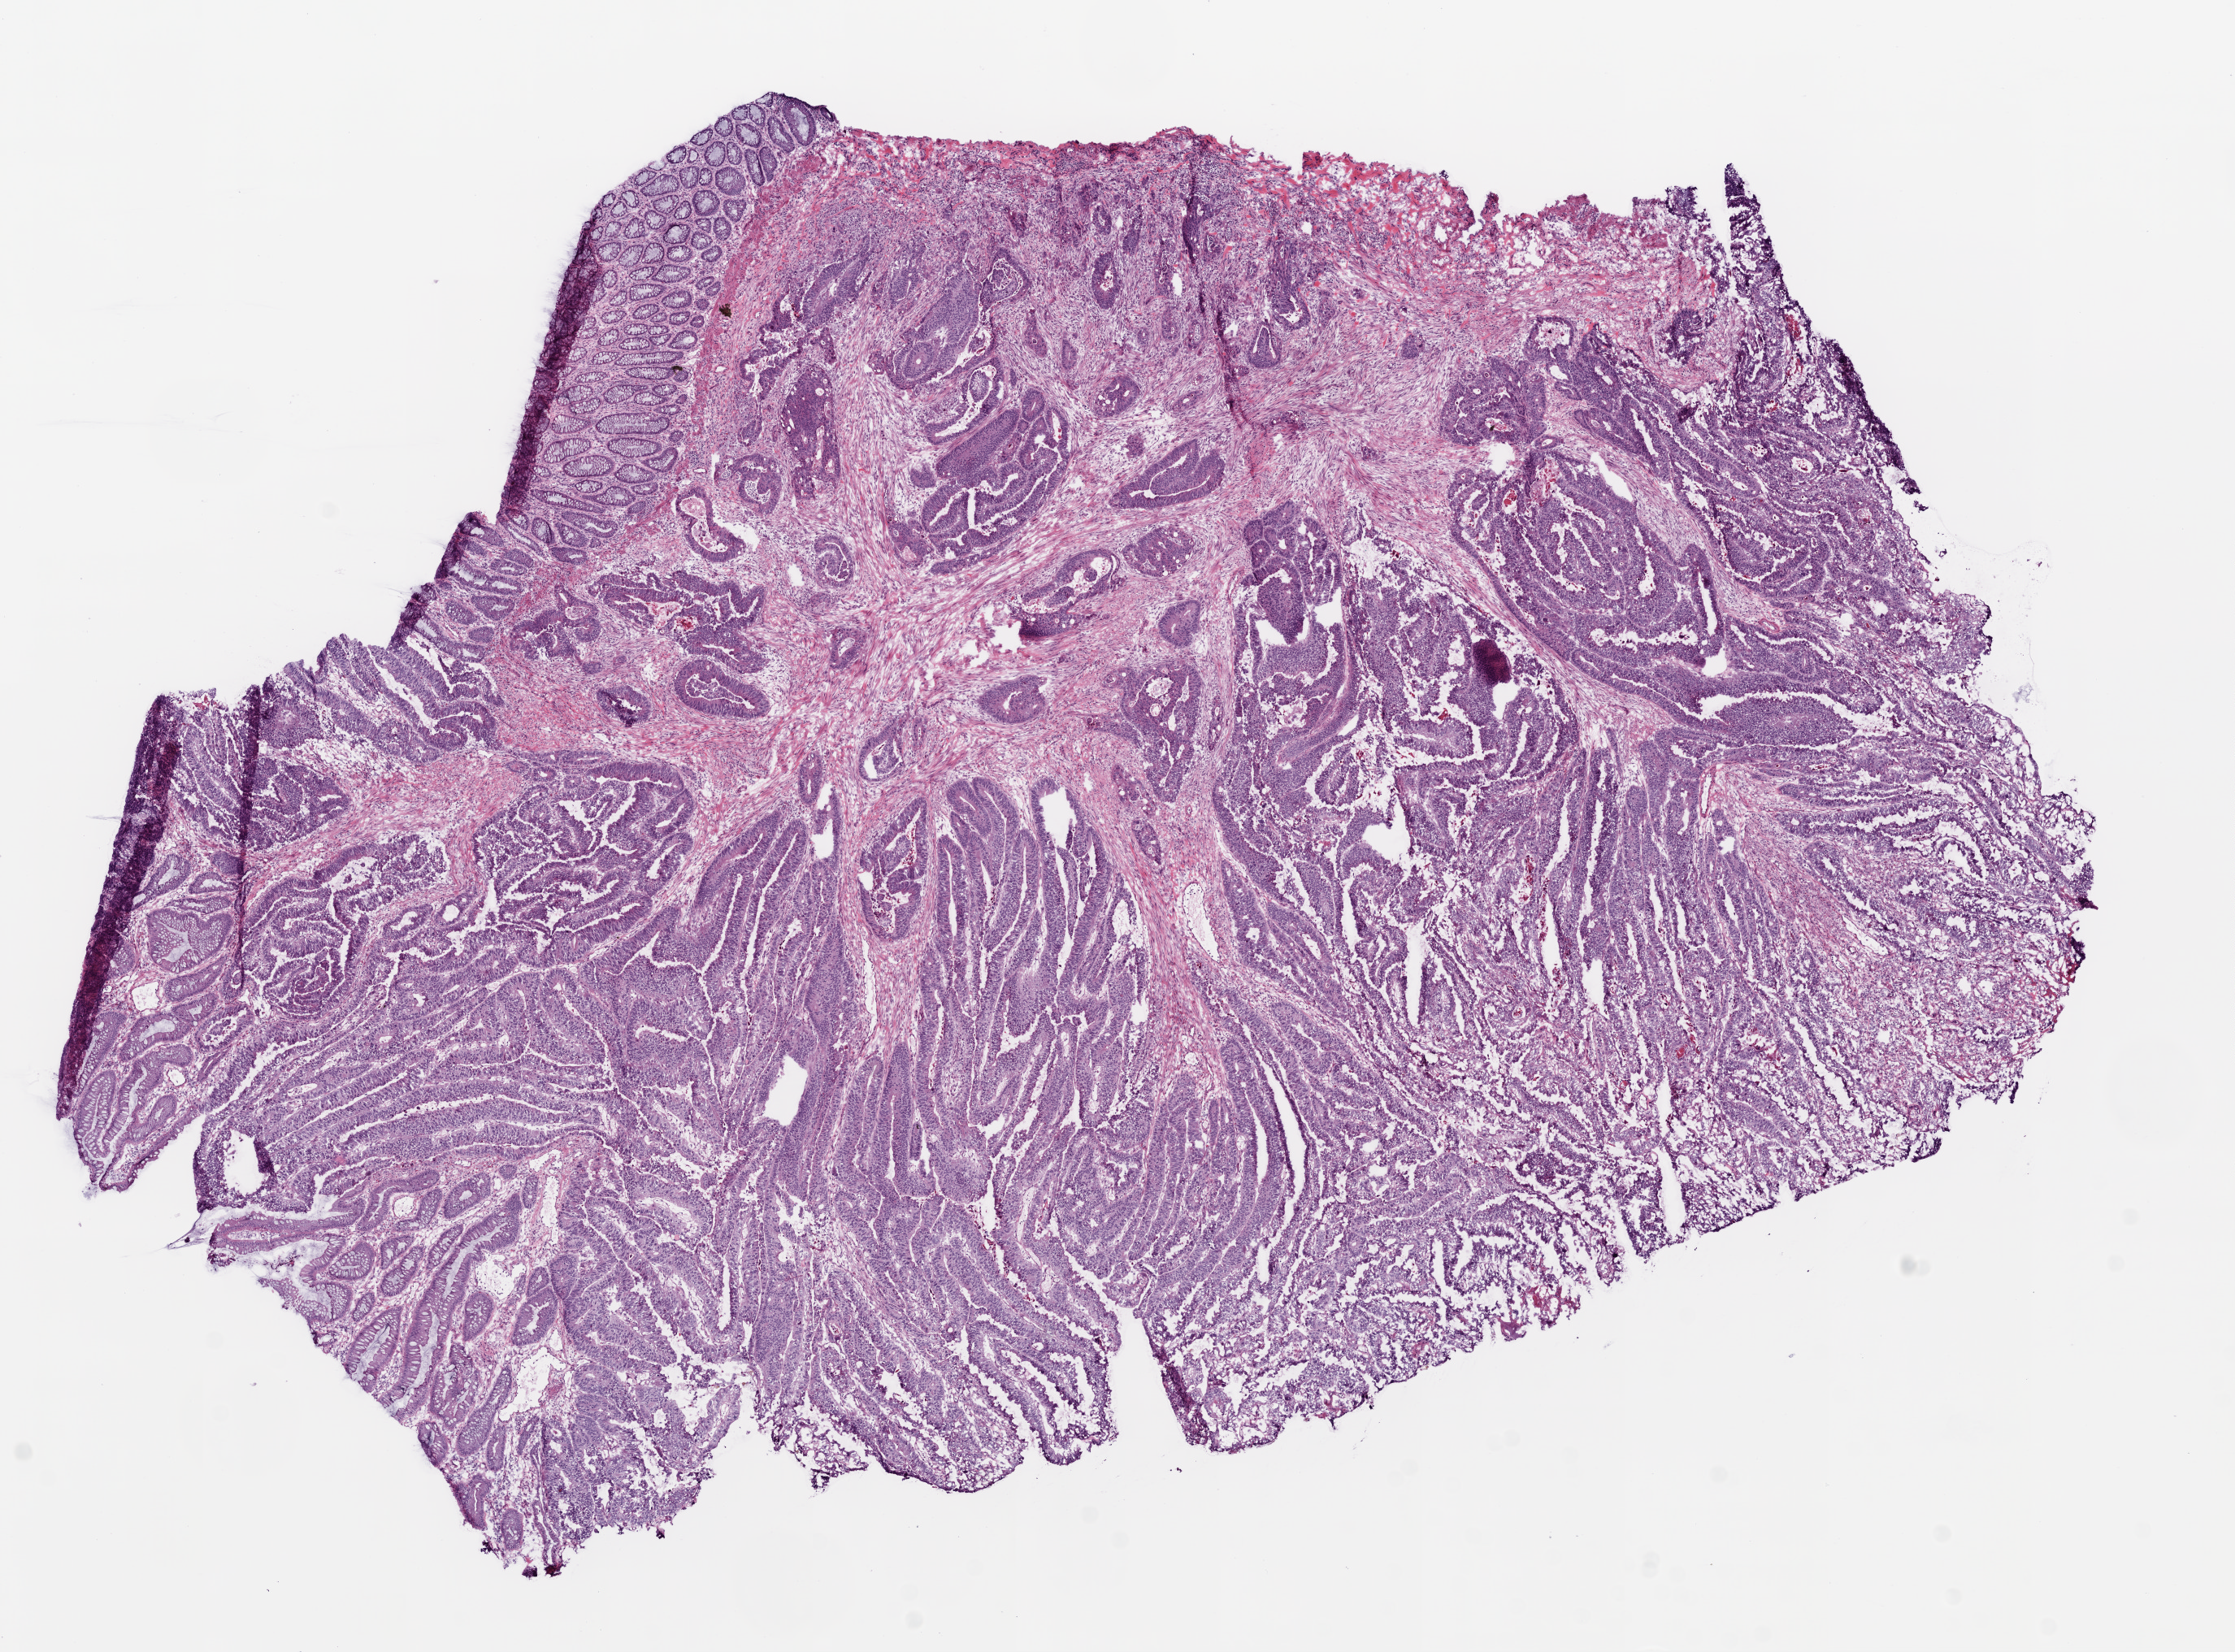
H&E-stained whole-slide image — whole scanned area (about 11.0 x 8.2 mm, slide scanned at 20x) shown as a low-resolution overview; frozen section from the bottom of the tissue portion; sample: primary tumour, colon. Male patient; age at initial diagnosis 72 years. Pathologist review of this section (percent, as recorded): tumour cells 70%, tumour nuclei 90%, normal cells 10%, stromal cells 20%, necrosis 0%.
Pathologic diagnosis: Adenocarcinoma, NOS. TNM: T3 N1 M1. AJCC pathologic stage: IV (6th edition).